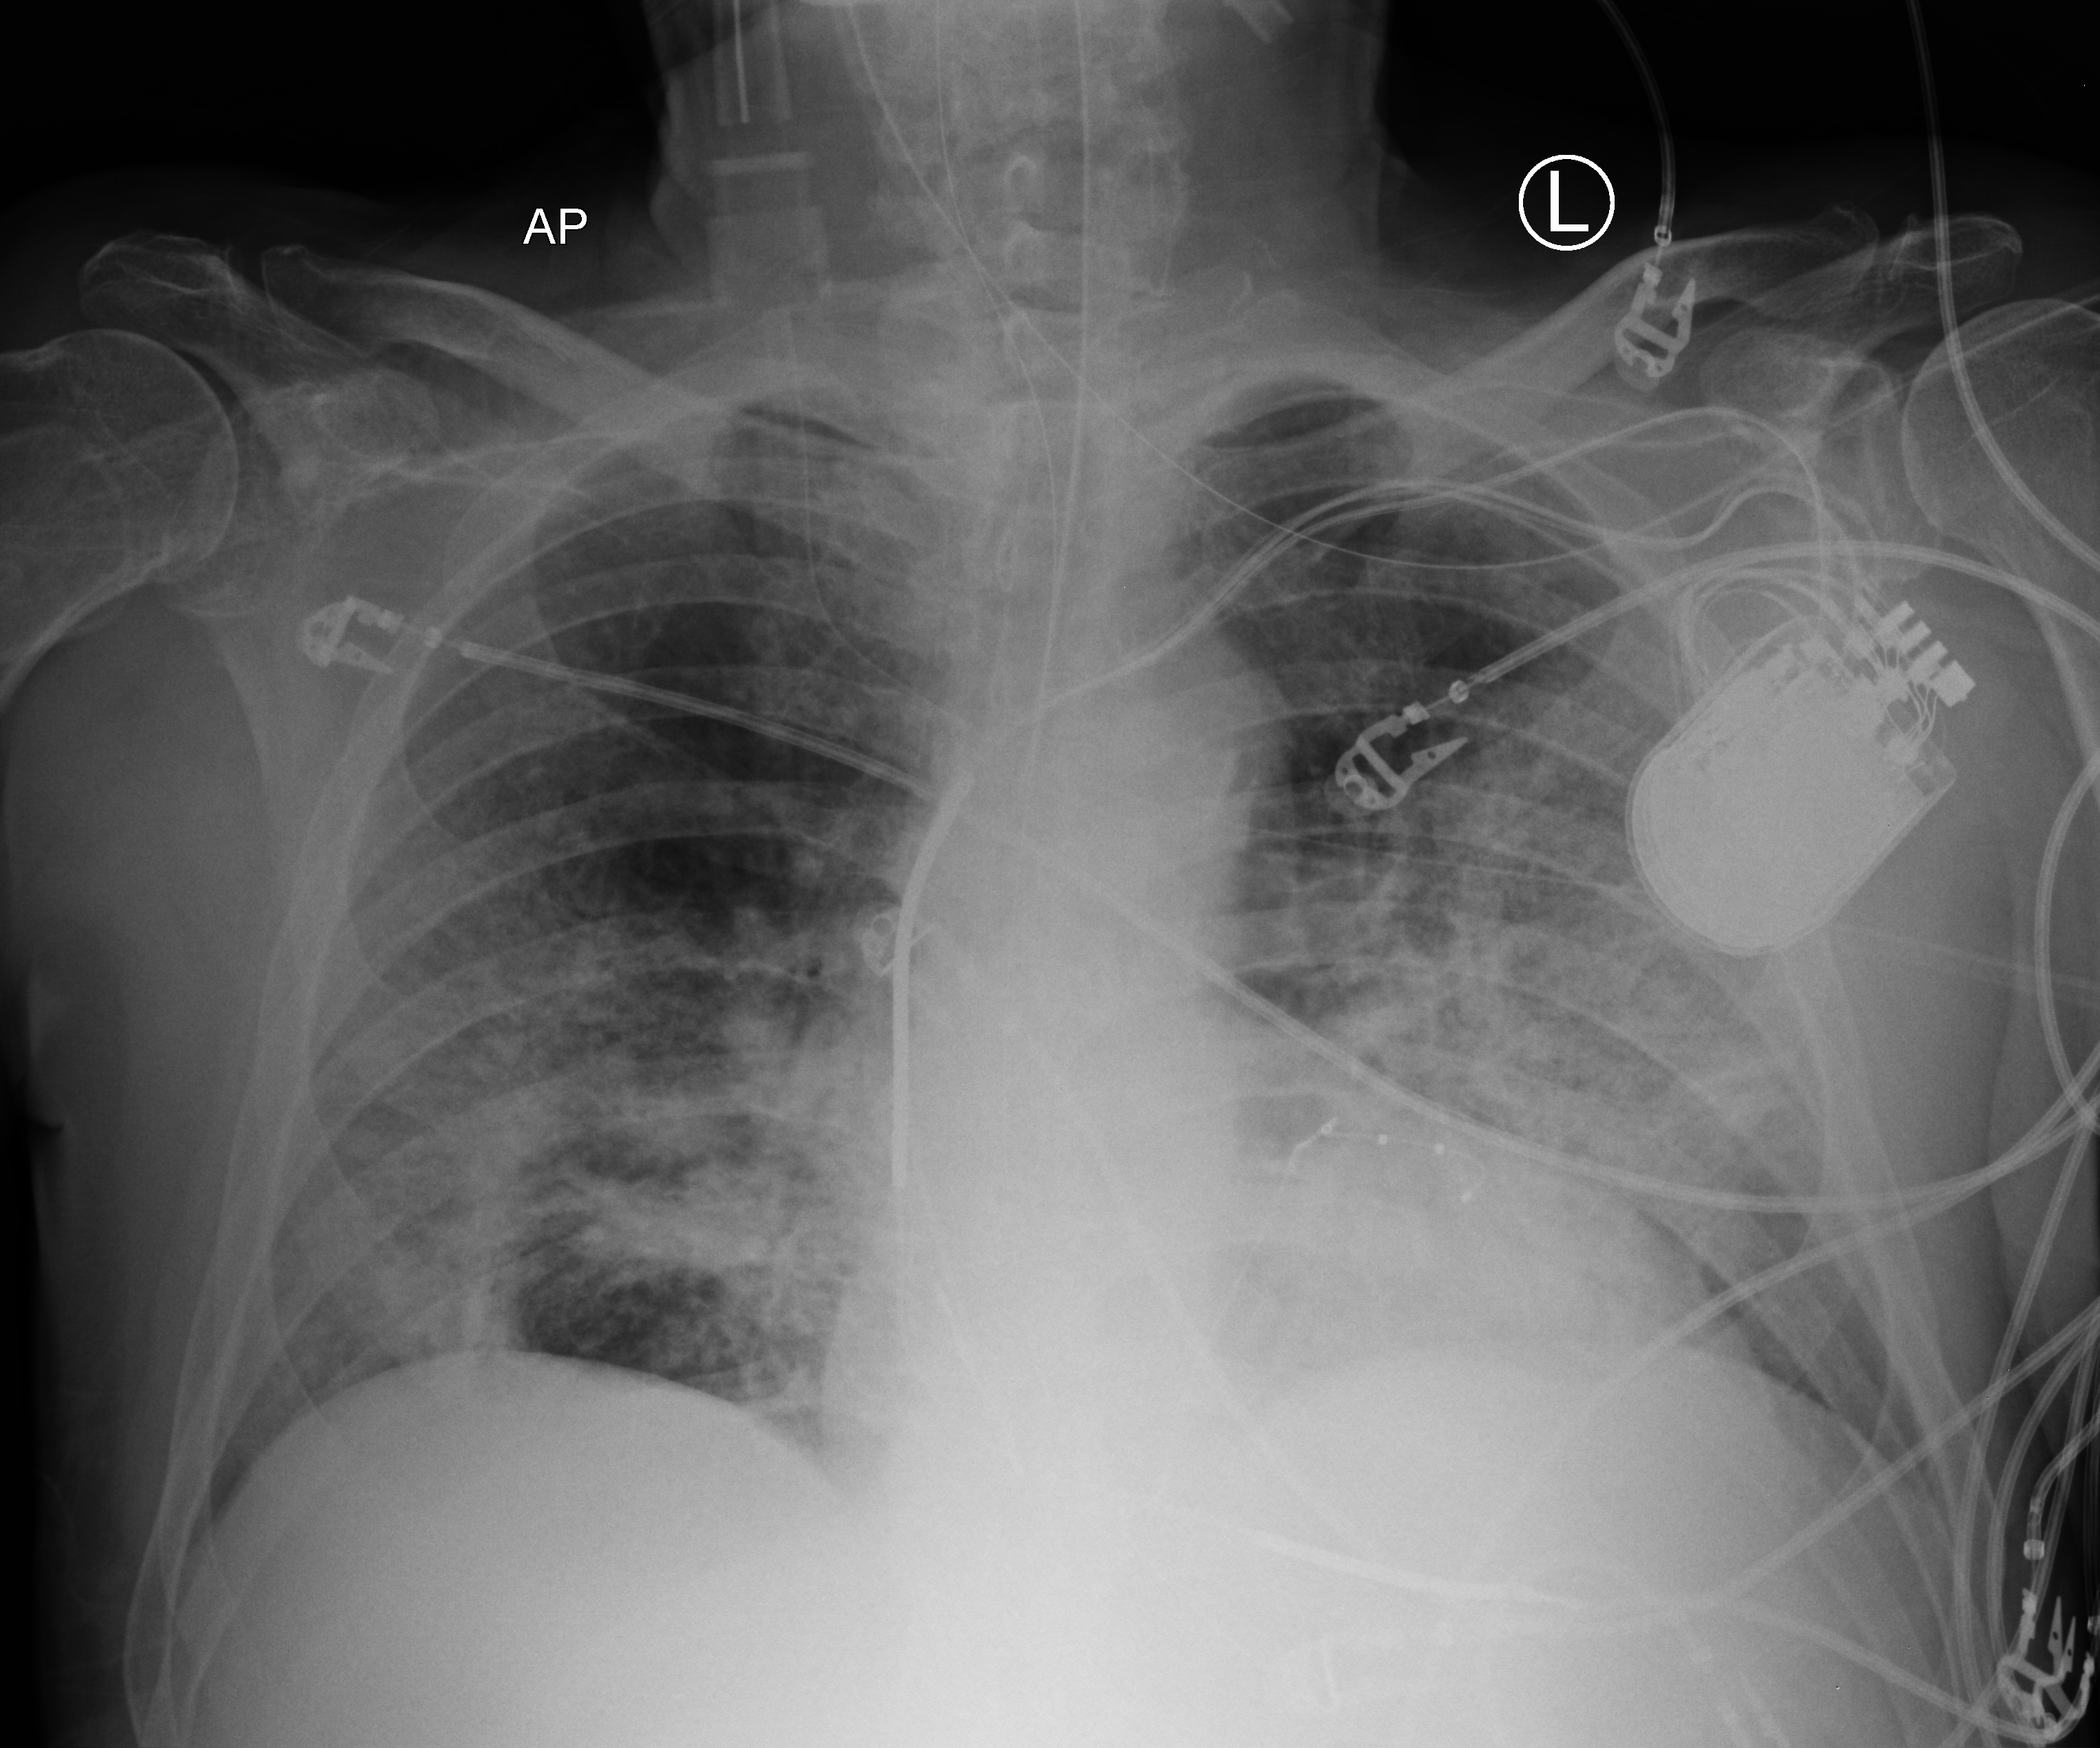
Portable chest radiograph. Male patient hospitalised with COVID-19, age 60–74 years.
Admission-level facts for this patient (not findings on this image; timing relative to this image not recorded): mechanically ventilated during this hospital stay: yes; admitted to intensive care during this hospital stay: yes; COPD (admission record): no.